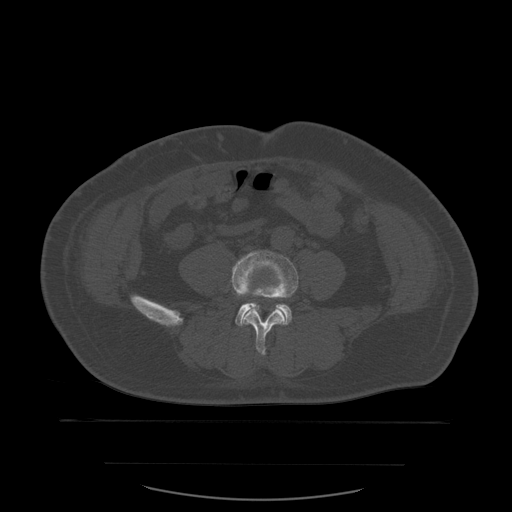
CT including the spine, one axial slice; position 155 of 590 along the scan axis; bone window (W 1800 / L 400 HU); 1.25 mm slice thickness; 512 × 512 image matrix, field of view 479 × 479 mm. Patient age 71 years. Case-level facts recorded for this patient, not image findings: primary cancer: lung.
Structures marked on this image (semi-automatically segmented with operator editing):
- L4 vertebra: bounding box (x1, y1, x2, y2) in pixels: (232, 251, 299, 356)
- L5 vertebra: (235, 297, 292, 327)